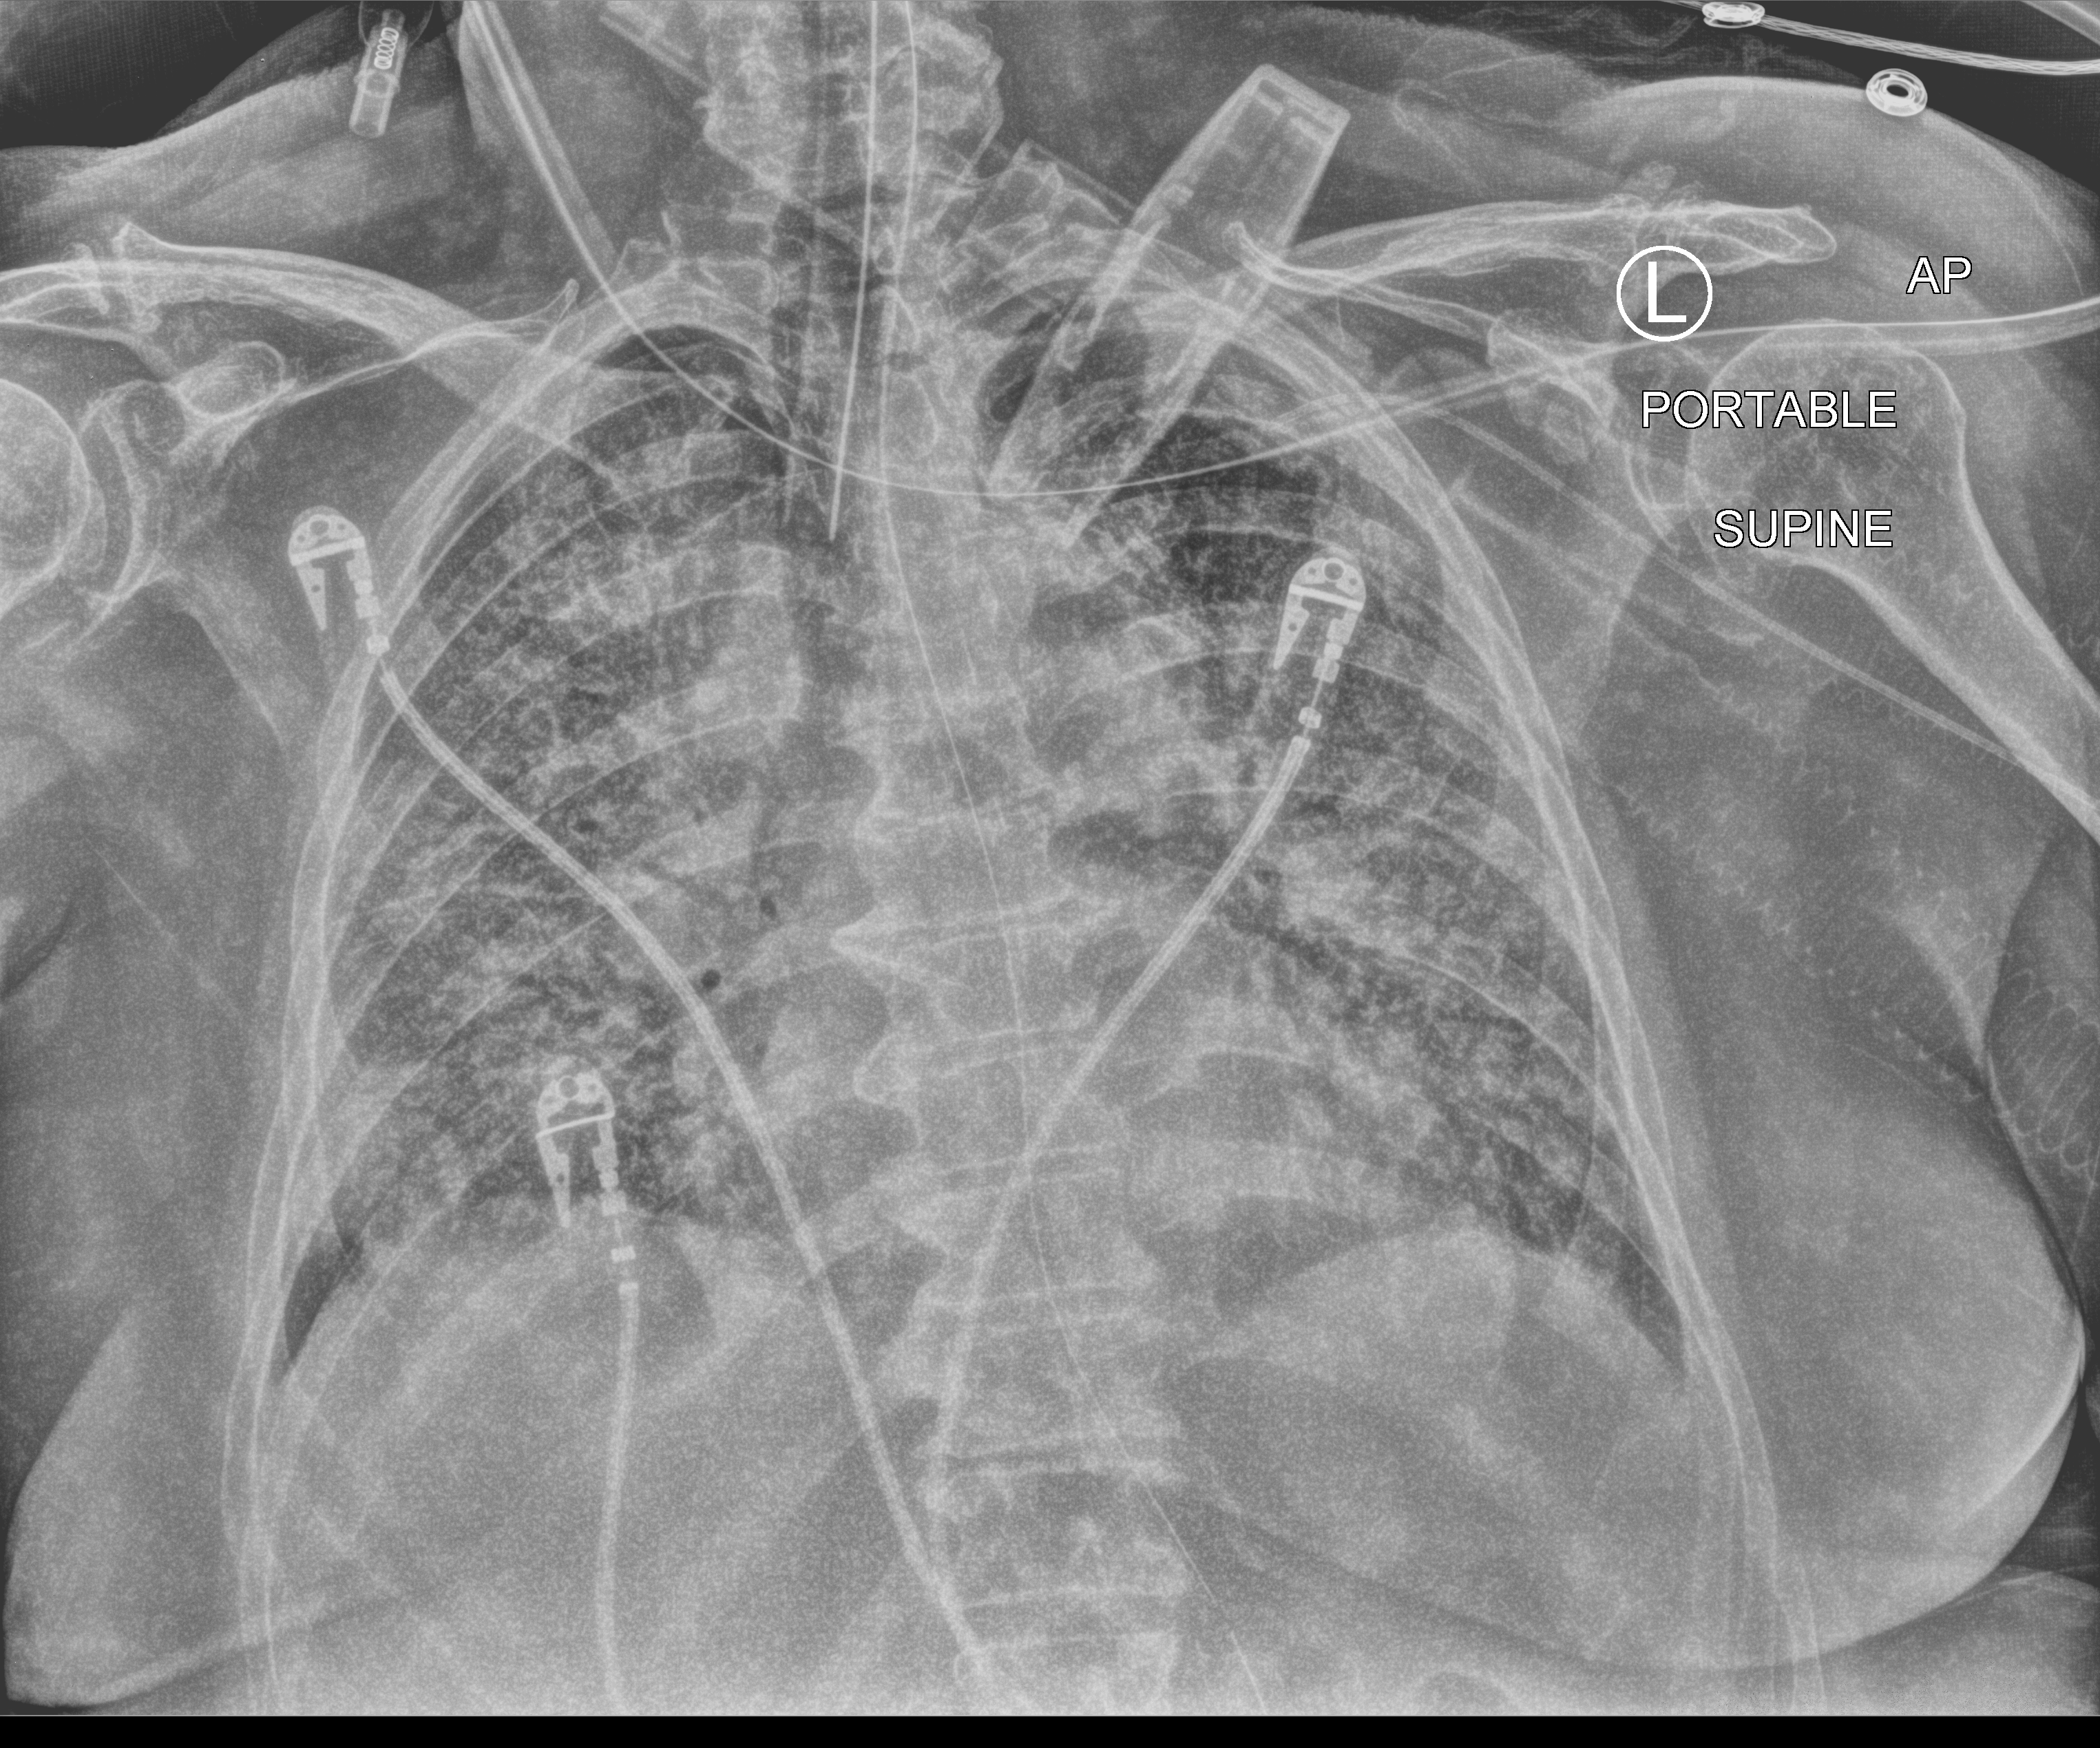
Bedside chest radiograph (computed radiography), anteroposterior (AP) projection. Patient hospitalised with COVID-19; female, aged 75–90 years.
From the hospital-stay record, not from the radiograph (when in the stay this image was taken is not recorded): hypertension (admission record): no.